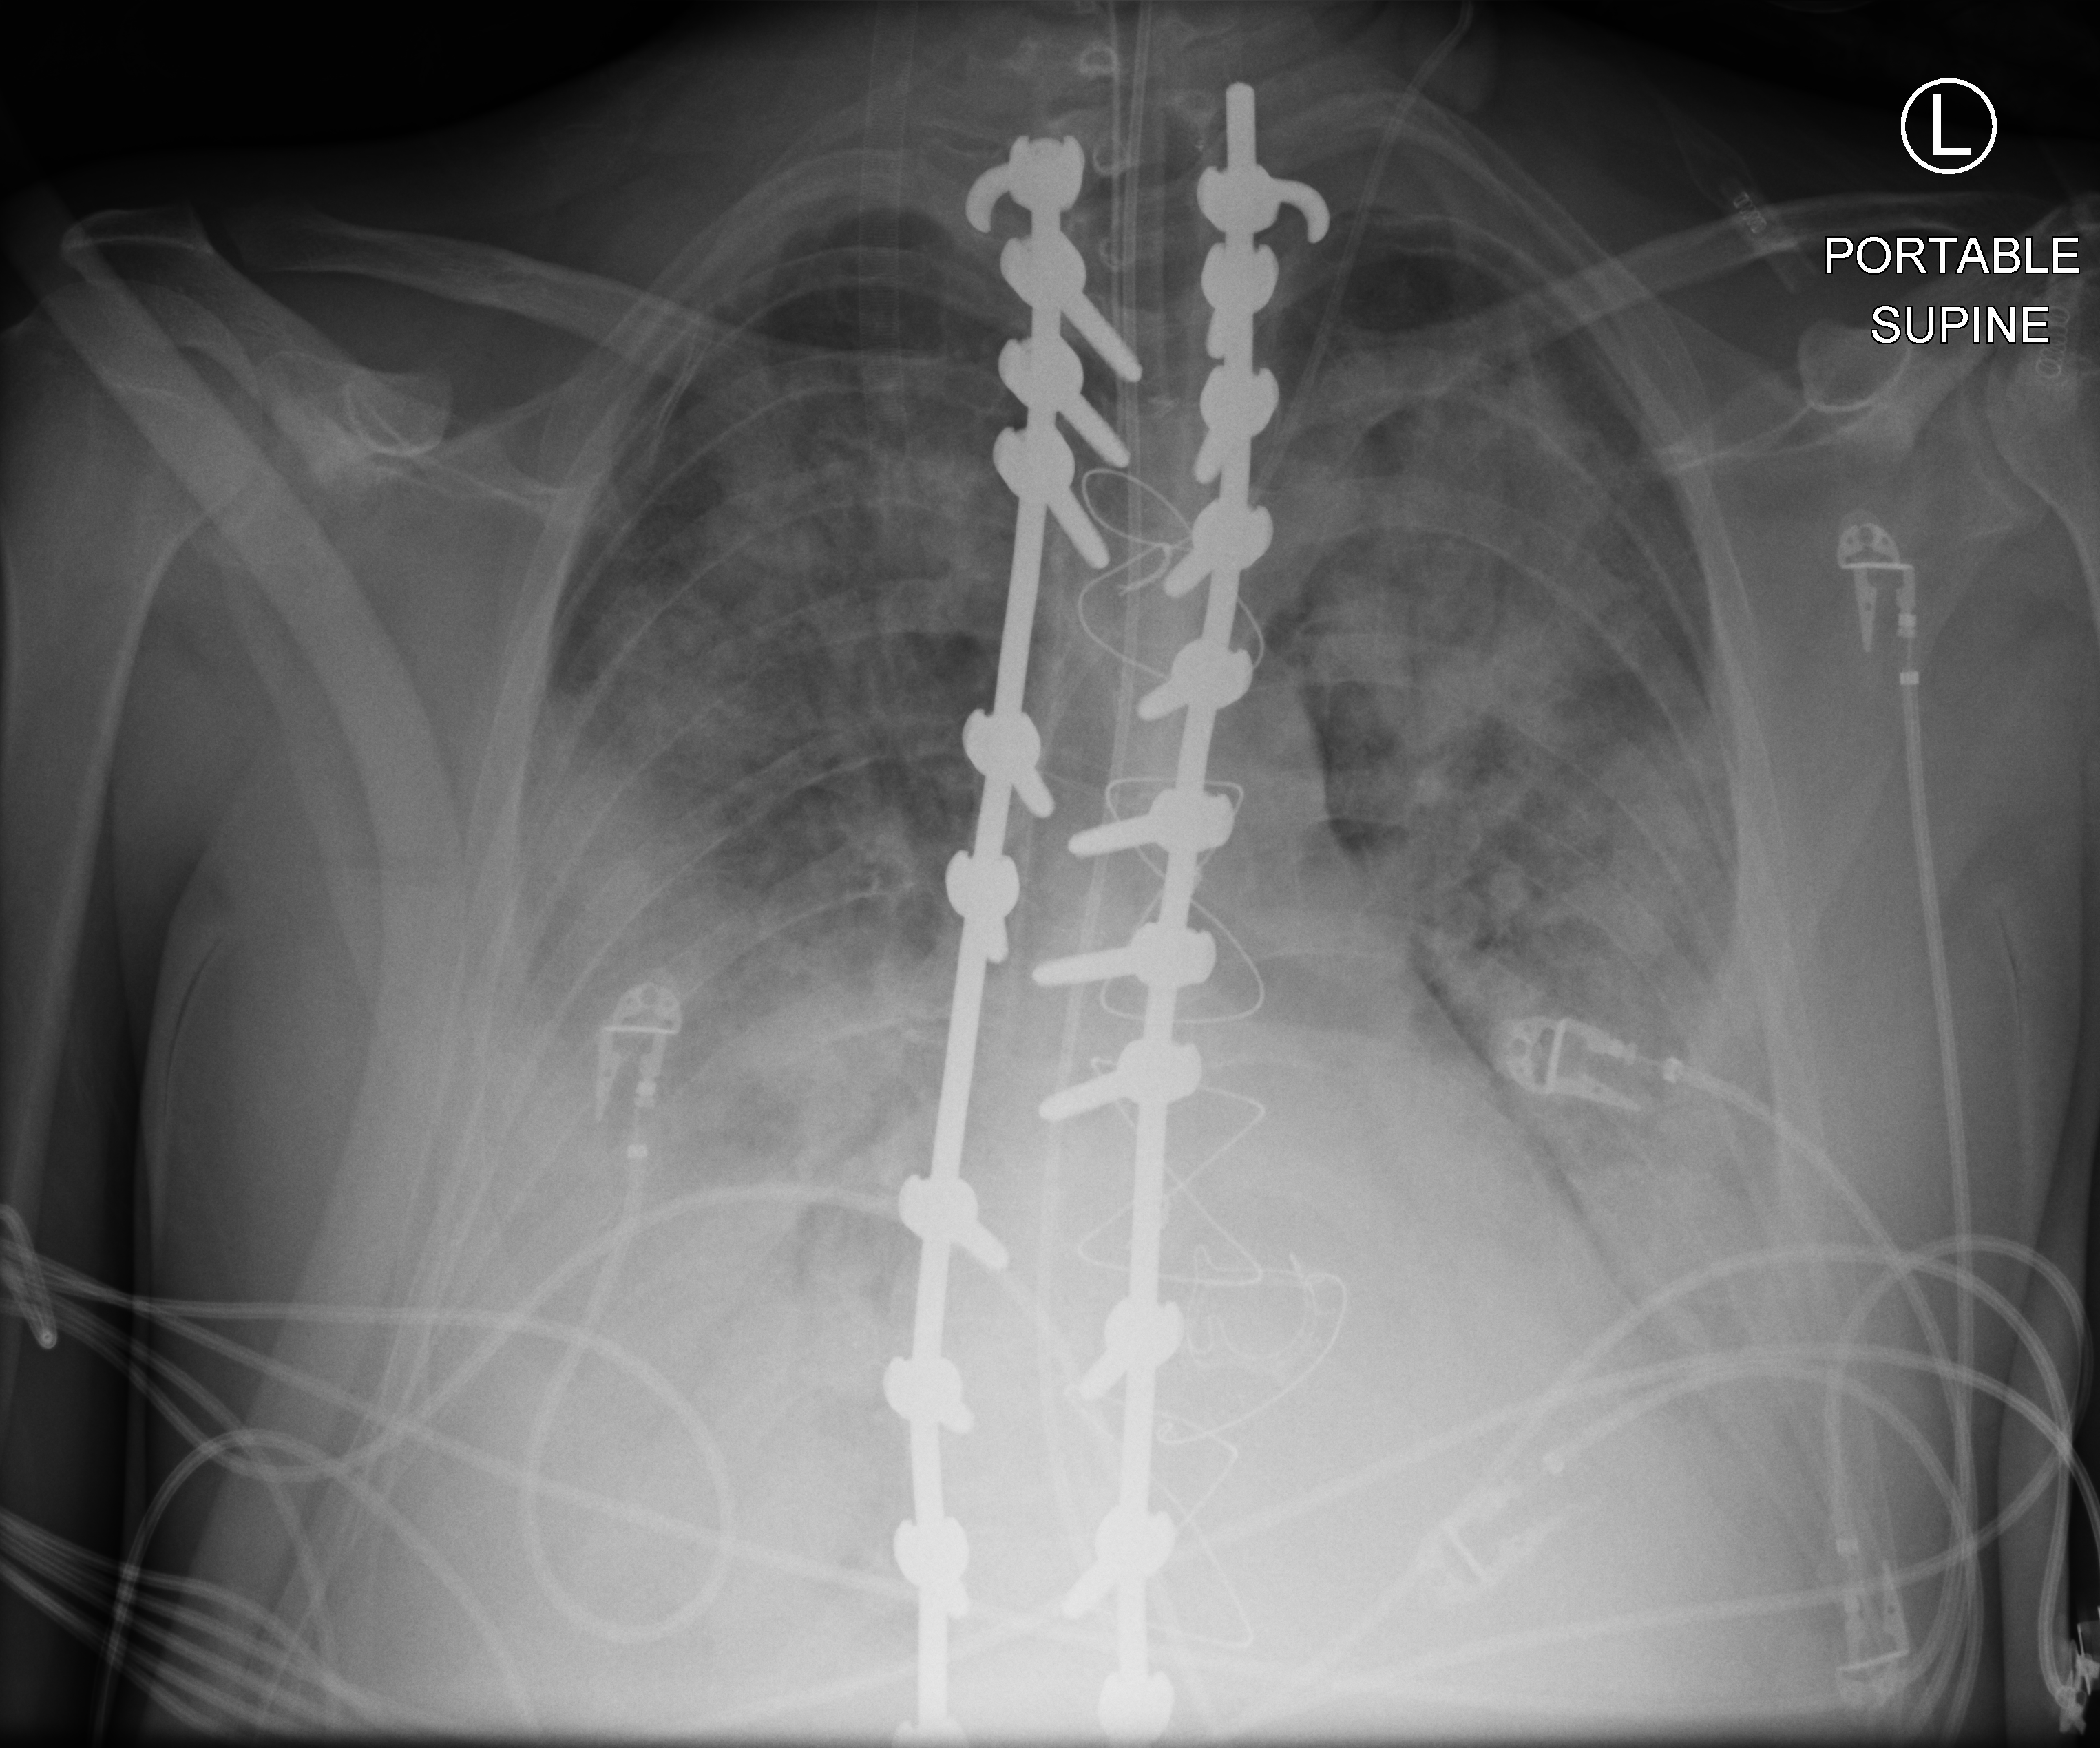
Portable chest radiograph; anteroposterior (AP) projection. Adult patient hospitalised with COVID-19, age 18–59 years.
Admission-level facts for this patient (not findings on this image; timing relative to this image not recorded):
- admitted to intensive care during this hospital stay: yes